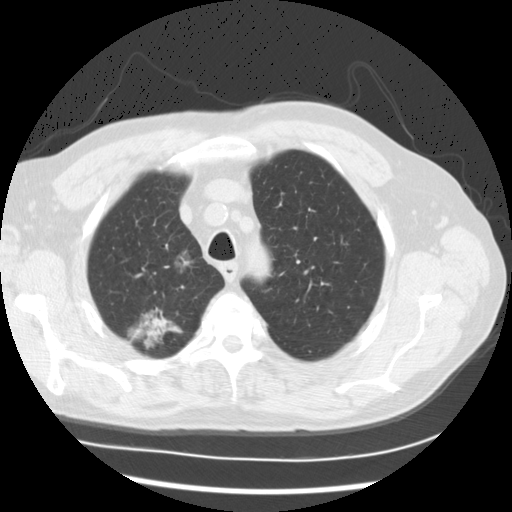
Axial slice from a low-dose chest CT screening exam; baseline screening round; lung window (W 1500 / L -600 HU). Male, age 68 years at enrolment. Current smoker at enrolment.
Expert-annotated lung lesion, bounding box <114,291,189,361> (left, top, right, bottom; pixels). The screening reader recorded 3 non-calcified nodules or masses ≥4 mm on this exam (right upper lobe, right upper lobe, right lower lobe); which of them this box marks is not recorded. Official screen result: positive, change unspecified: nodule(s) >= 4 mm or enlarging nodule(s), mass(es), or other non-specific abnormalities suspicious for lung cancer. Later outcome: lung cancer diagnosed 90 days after this screen — adenocarcinoma, NOS, right upper lobe, right lower lobe, well differentiated (G1), stage IV (AJCC 6th edition), 35 mm at pathology.